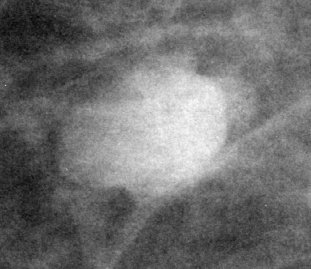
Region of interest cut from a scanned film mammogram (one marked finding), right breast, CC view, BI-RADS breast density category 2 (scale 1–4).
Marked abnormality: mass, shape lobulated, margins circumscribed; BI-RADS assessment category 4; pathology result (as recorded, not read from the image): benign.